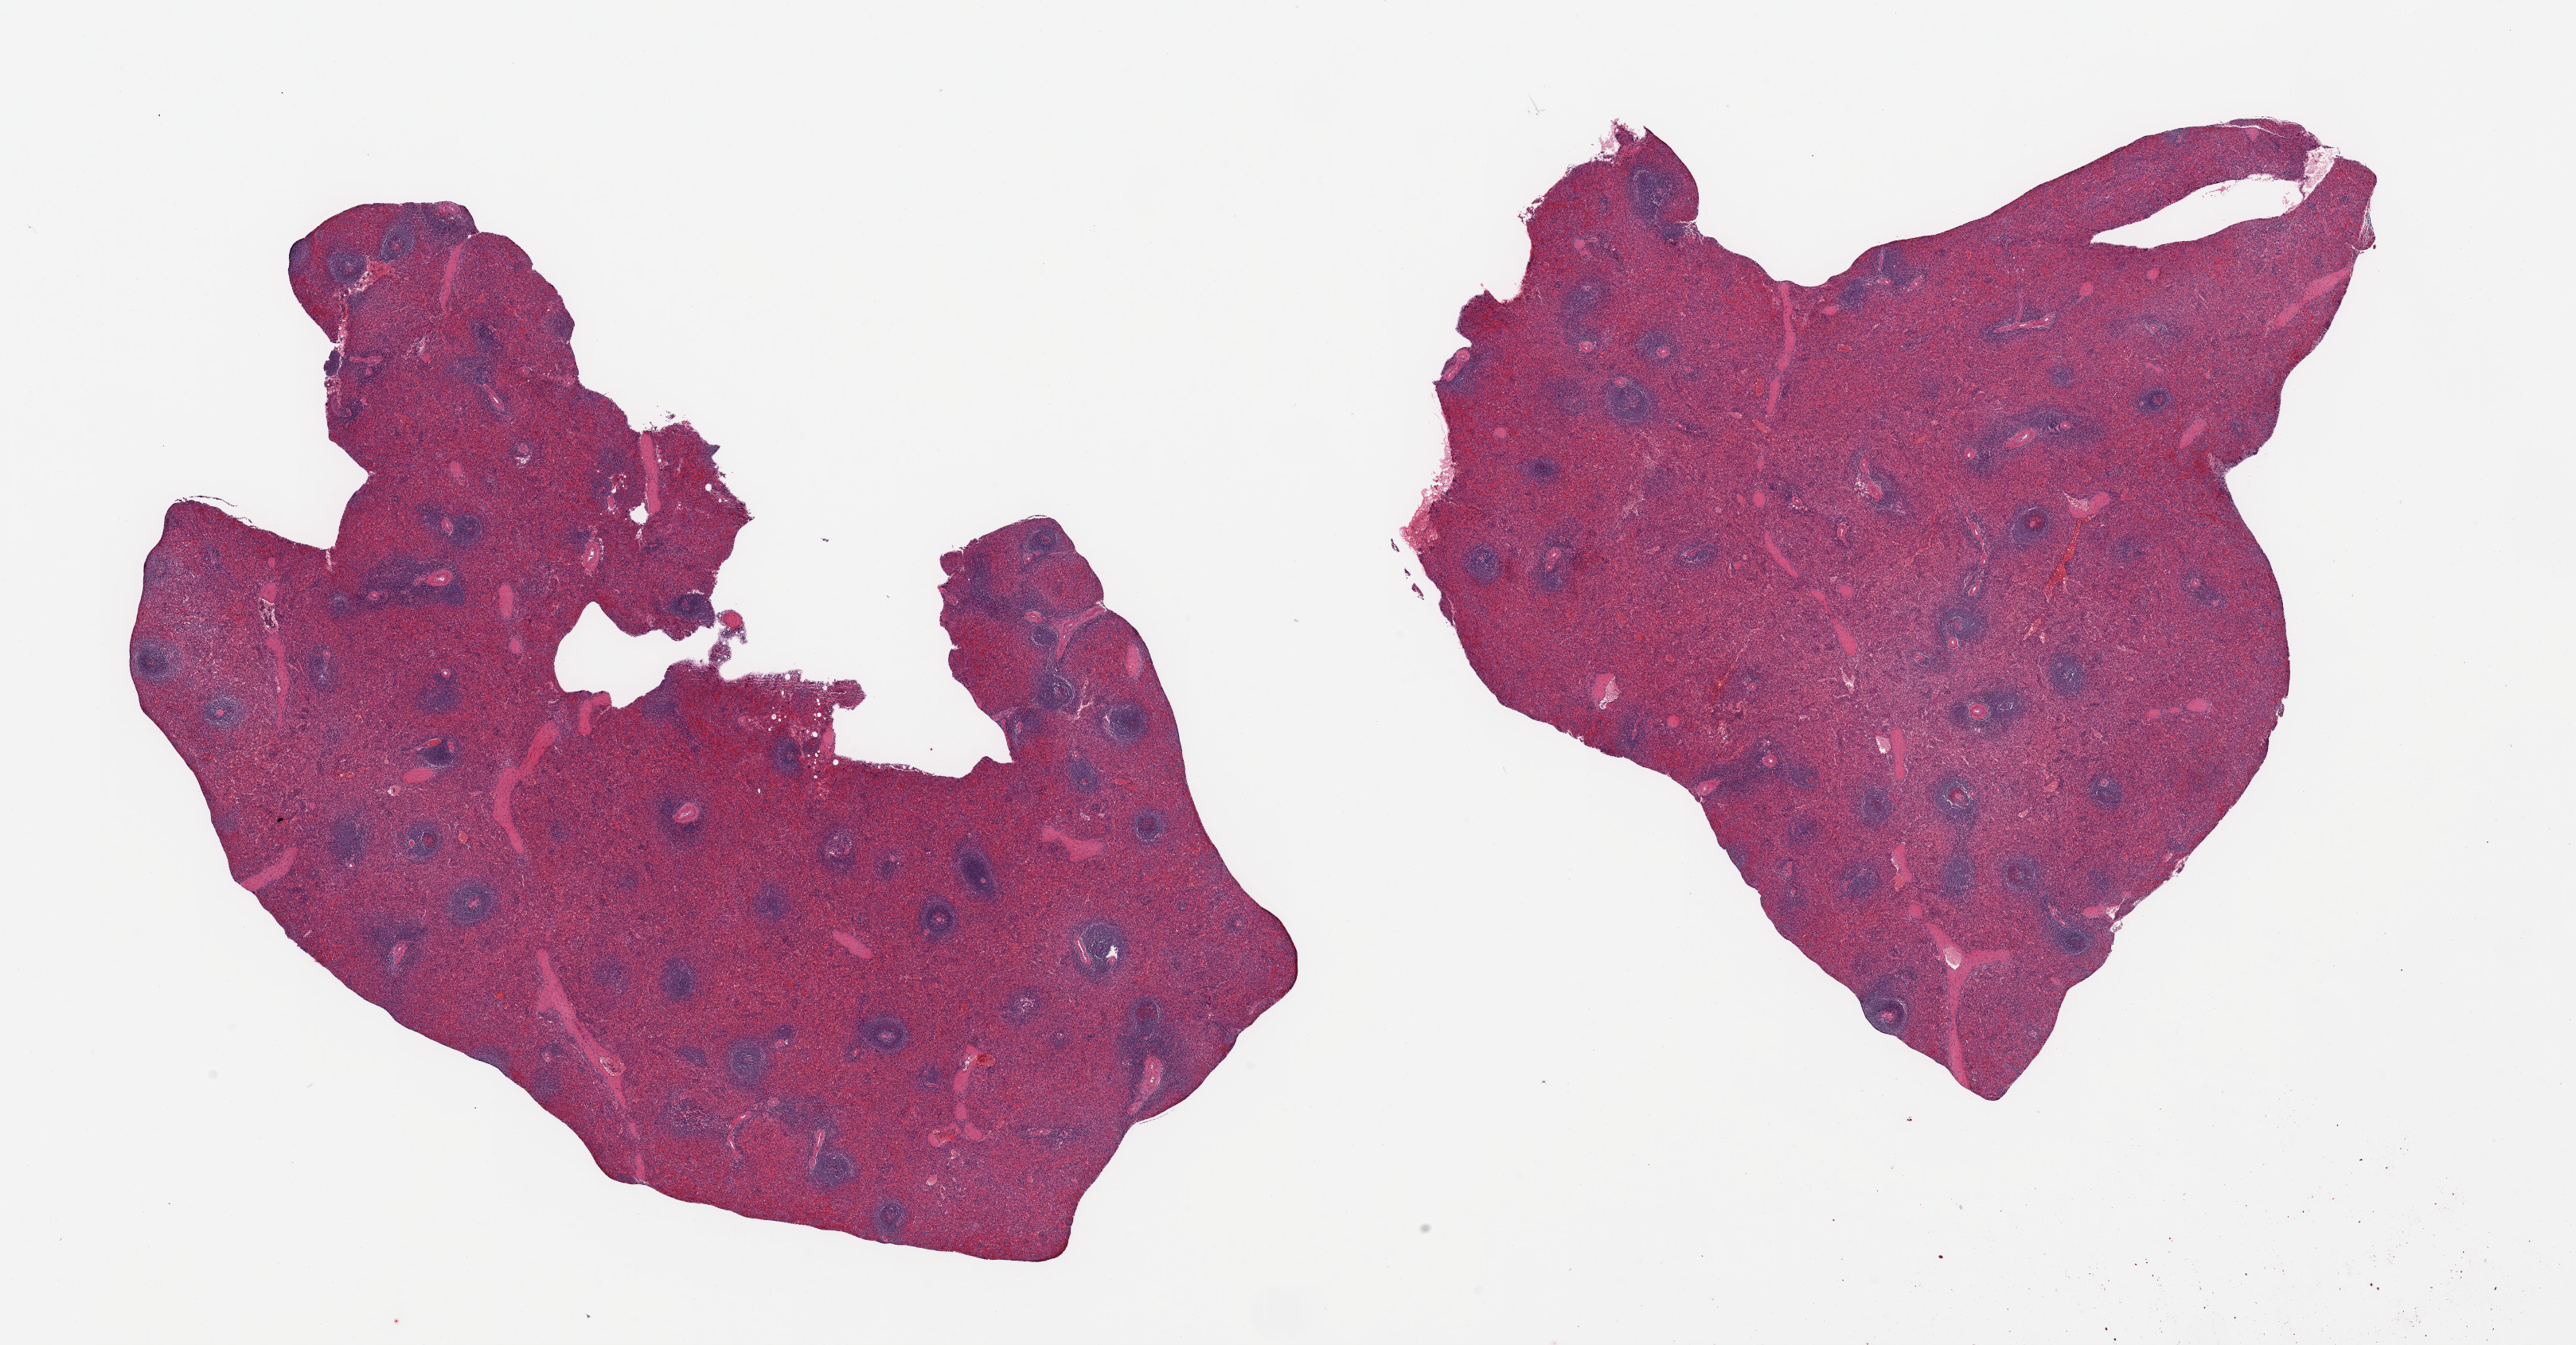
Whole-slide image, H&E stain — shown as a low-resolution overview of the whole scanned area (about 25.6 x 13.4 mm, acquisition: 20x scan); PAXgene-fixed, paraffin-embedded tissue; section of spleen (target tissue); tissue donor sample. Donor sex: male.
Reviewer comment on this tissue sample: 2 pieces.